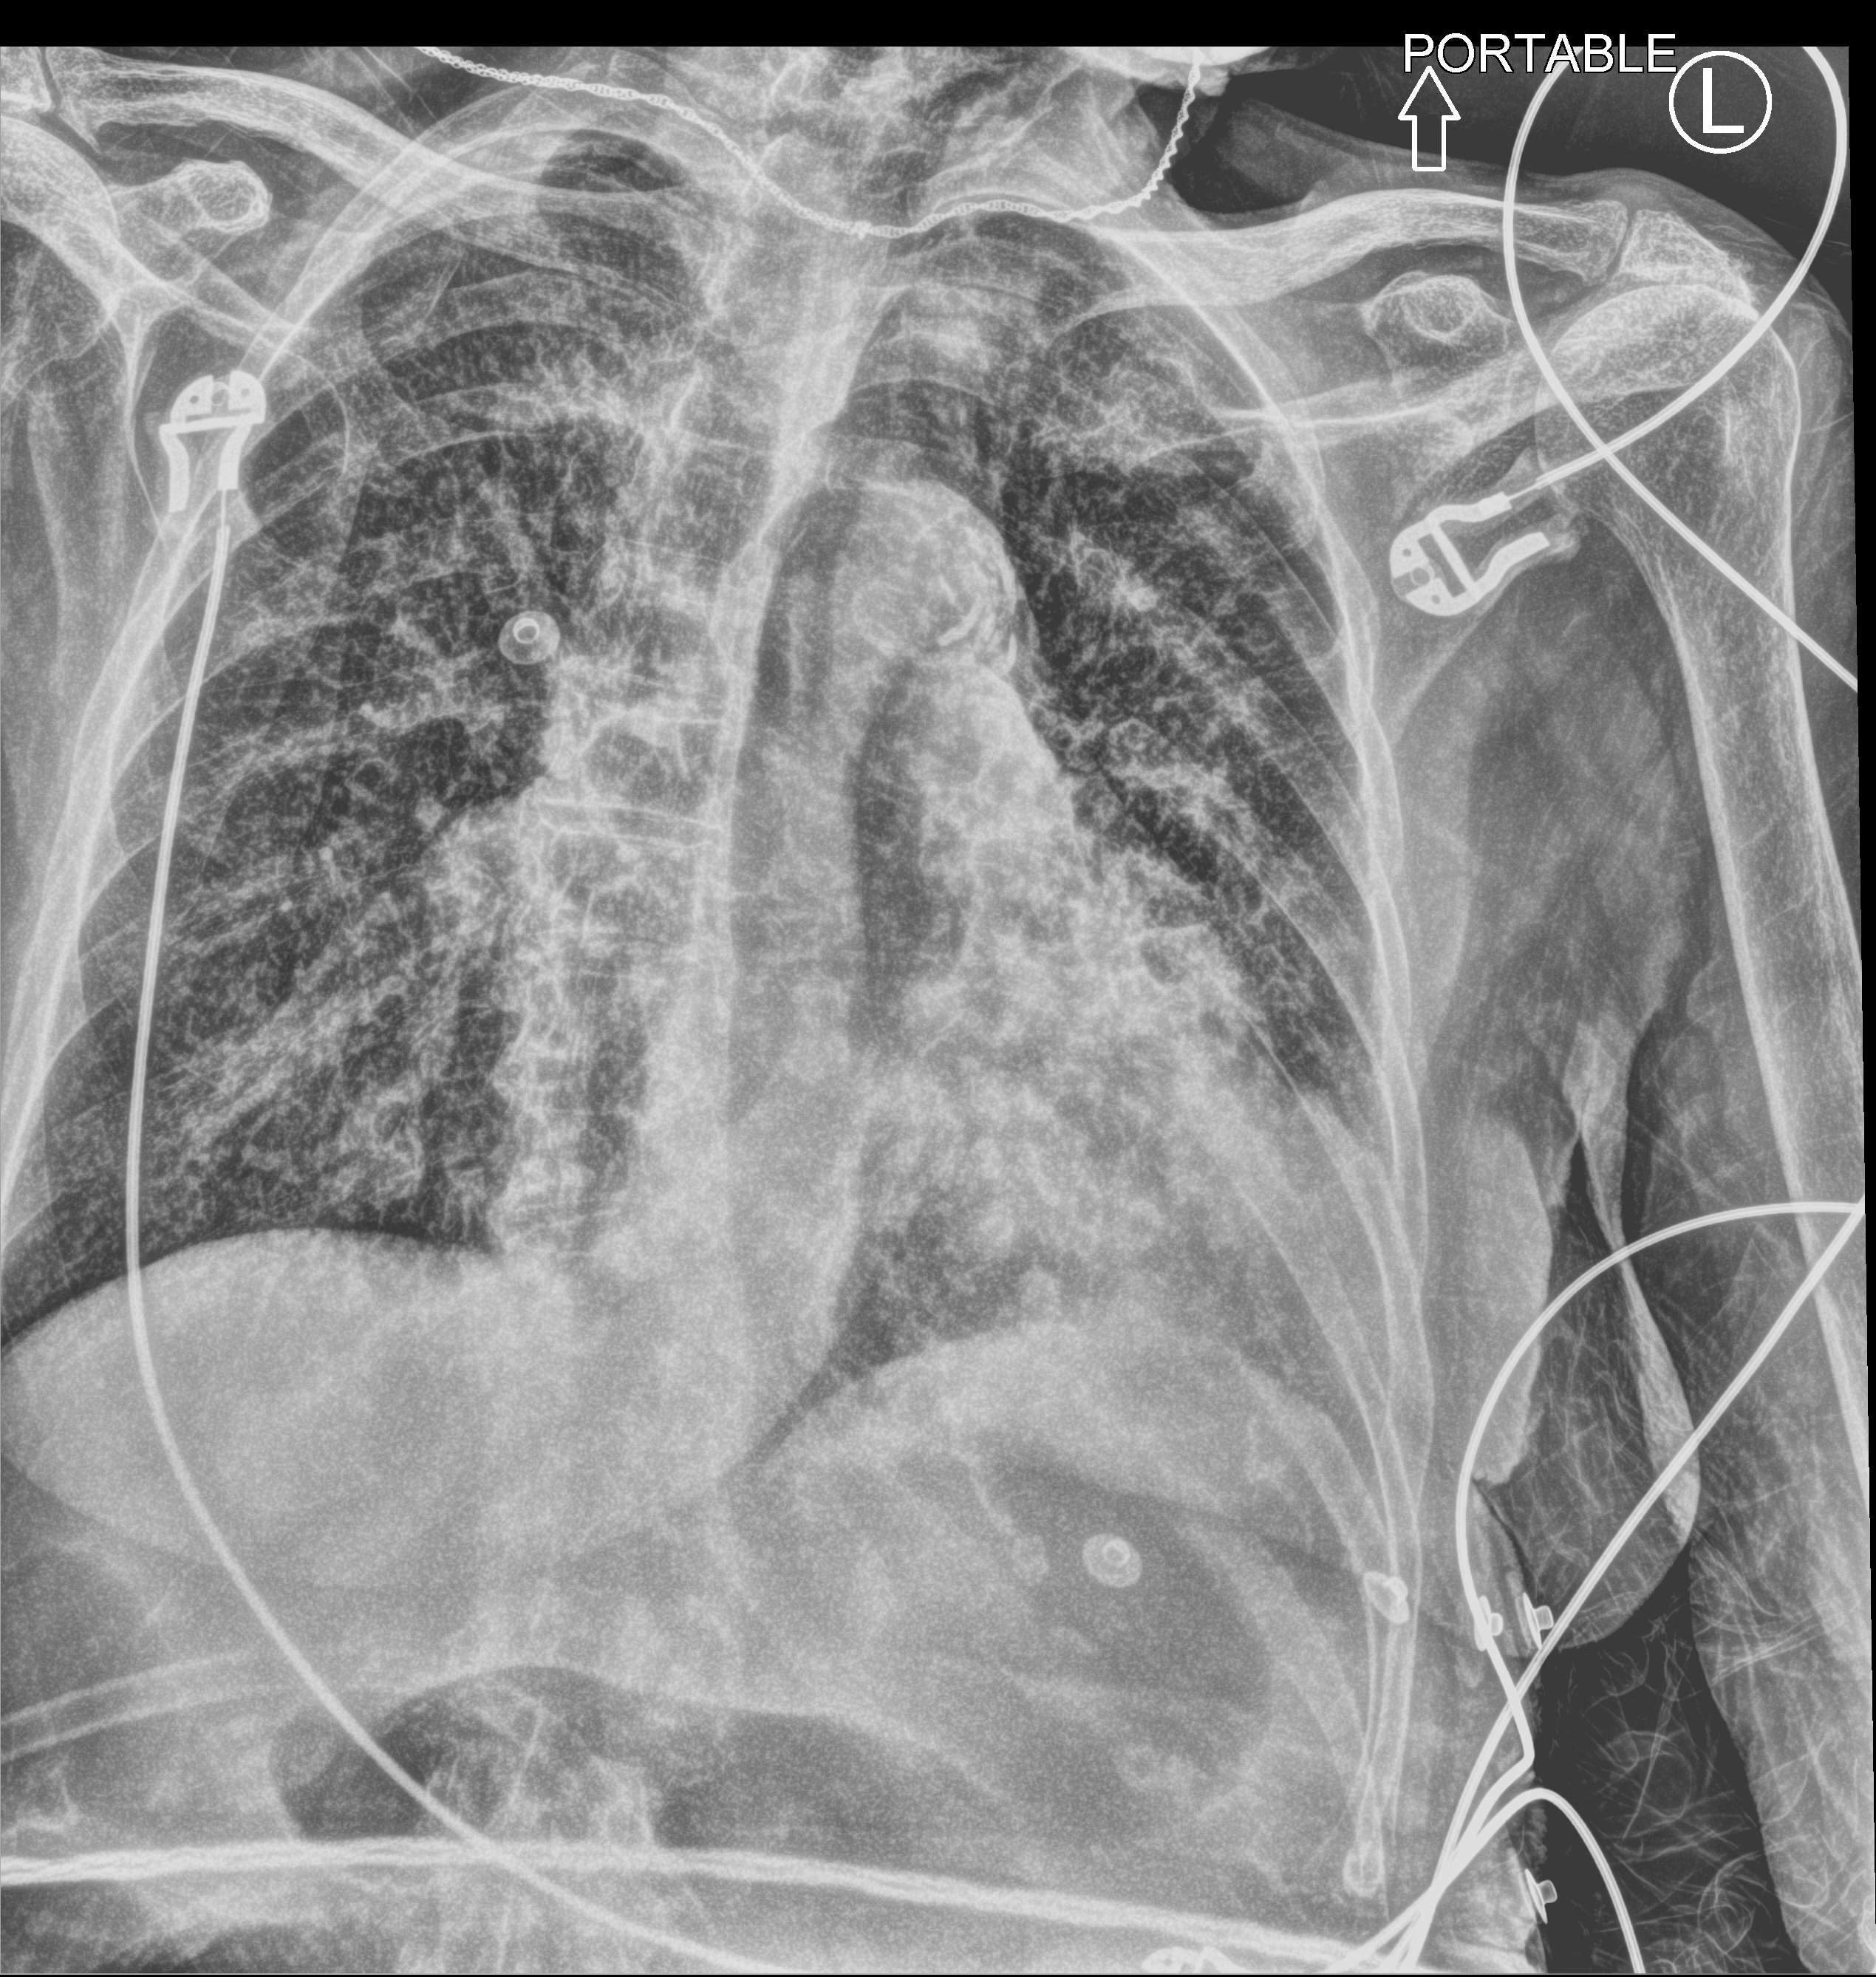
Bedside chest radiograph (computed radiography). Female patient hospitalised with COVID-19, age 75–90 years.
From the hospital-stay record, not from the radiograph (when in the stay this image was taken is not recorded): smoking status (admission record): former; mechanically ventilated during this hospital stay: no.